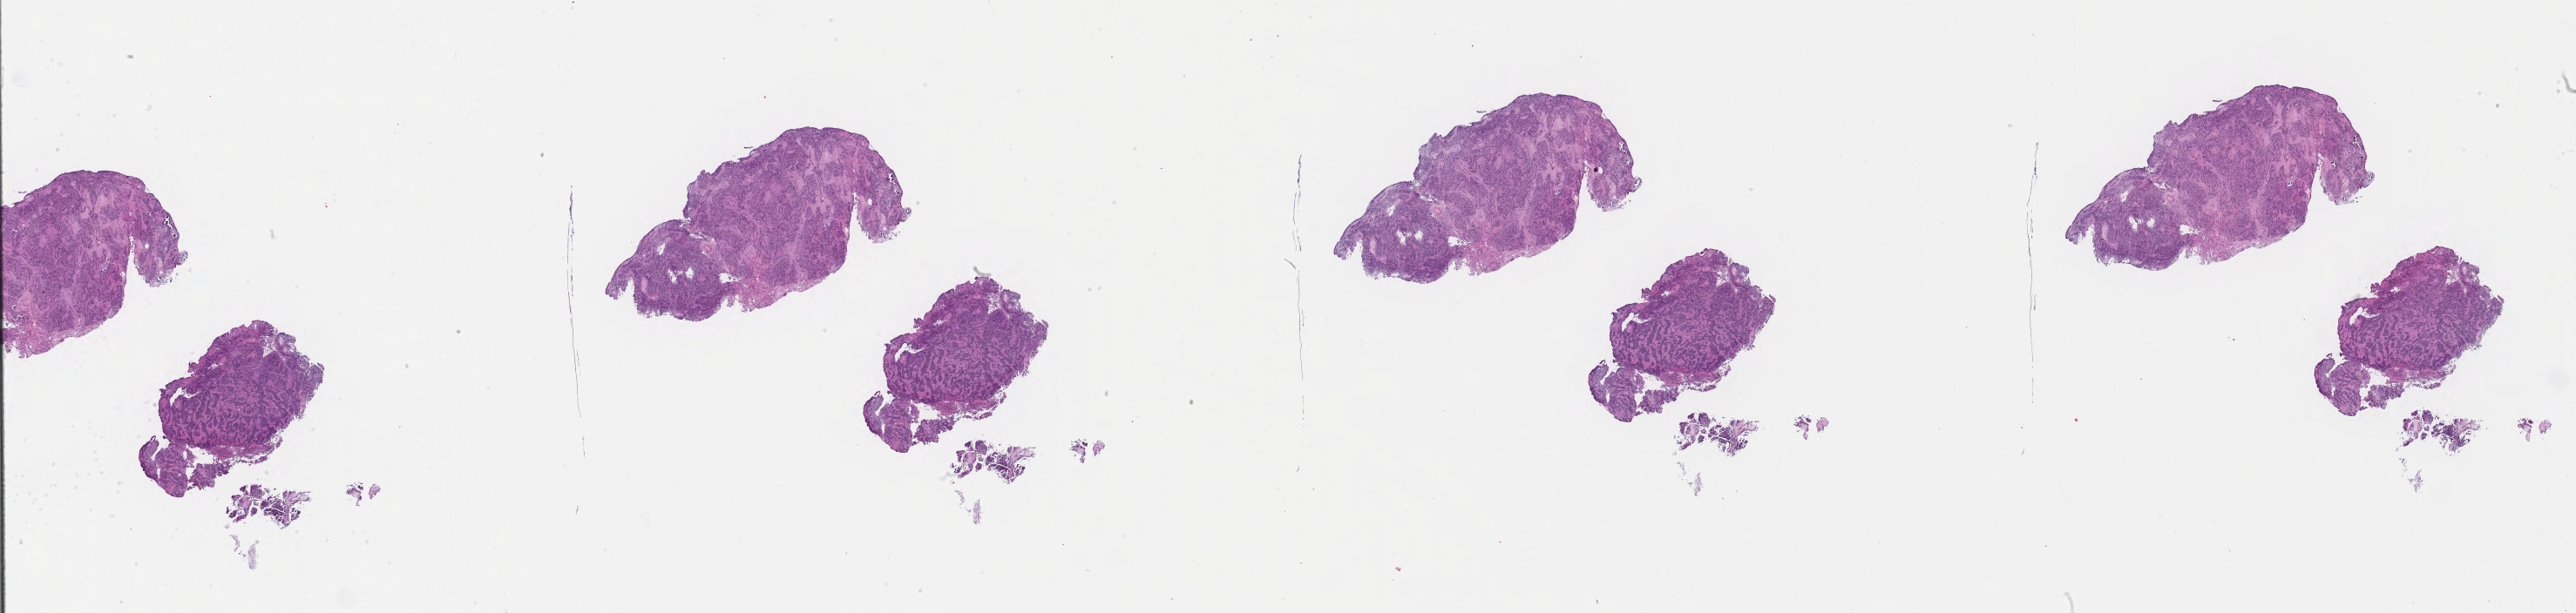
Whole-slide image, haematoxylin and eosin stain of tumor tissue from the brain, low-resolution overview of the scanned area, about 47.8 x 11.4 mm, FFPE section. Male patient, age 123 months (10 years 3 months).
Diagnosis (ICD-O-3 morphology term): Neoplasm, uncertain whether benign or malignant.